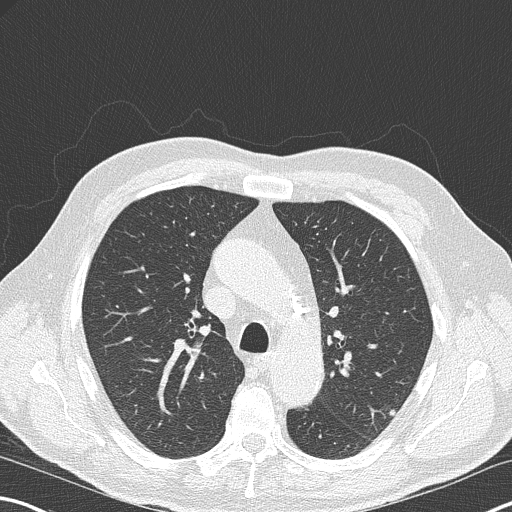
Low-dose screening chest CT, axial slice. Second annual screen. Lung window (W 1500 / L -600 HU). 512 × 512 image matrix. Male participant, aged 67 years at enrolment. Former smoker at enrolment.
Lesion marked by an expert reader, bounding box (x1, y1, x2, y2) in pixels: (368, 397, 410, 428). Screening reader's record for this exam (one nodule recorded; not confirmed to be the boxed lesion): non-calcified nodule or mass ≥4 mm, left upper lobe, 9 × 6 mm, poorly defined margins, soft tissue attenuation, pre-existing on the prior screen: no. Participant outcome: lung cancer diagnosed 418 days after this screen (after the third annual screen) — squamous cell carcinoma, large cell, nonkeratinizing, NOS, left upper lobe, moderately differentiated (G2), stage IA (AJCC 6th edition), 15 mm at pathology.